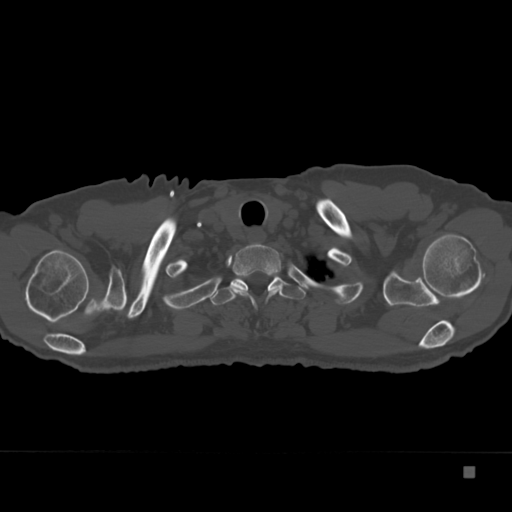
CT including the spine, one axial slice. Reconstruction kernel Br40s. 120 kVp. Bone window (W 1800 / L 400 HU). 1.5 mm slice thickness. 512 × 512 image matrix, field of view 389 × 389 mm. Male patient, age 72 years. Case-level facts recorded for this patient, not image findings: primary cancer: skeletal.
Structures marked on this image (semi-automatically segmented with operator editing):
- T1 vertebra: box from (x=230, y=243) to (x=281, y=306) px
- T2 vertebra: (x=210, y=273)–(x=306, y=305)